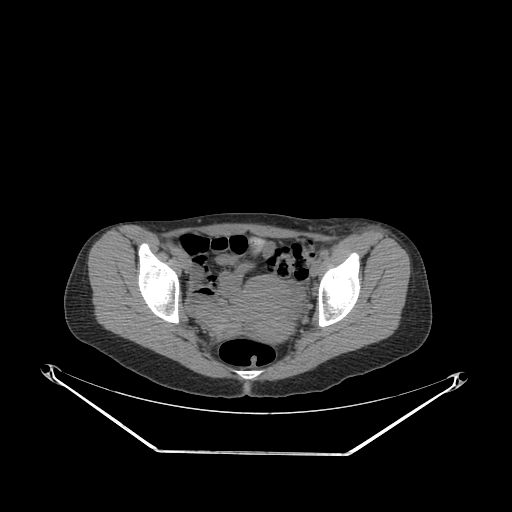
CT of an extremity soft-tissue mass (from a PET/CT study), one axial slice. Position 79 of 267 along the scan axis. Reconstruction kernel SOFT. Soft-tissue window (W 400 / L 40 HU). 512 × 512 image matrix. Female patient. From the clinical record (not read from this slice): histological type: leiomyosarcoma; grade: high; site of the primary tumour: groin.
Outlined on this slice (expert contour drawn on MRI and transferred to this co-registered scan by the dataset authors):
- gross tumour volume including surrounding oedema: bounding box (x1, y1, x2, y2) in pixels: (320, 233, 394, 257)
- gross tumour volume (mass): (329, 246, 343, 252)